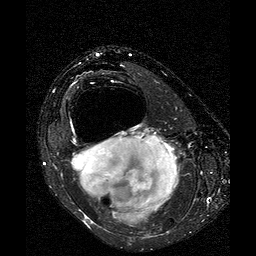
MRI of an extremity soft-tissue mass, one axial slice; position 20 of 25 along the scan axis; T2-weighted fat-saturated; 256 × 256 image matrix, field of view 160 × 160 mm. Female patient. Case-level facts recorded for this patient, not image findings: histological type: liposarcoma; site of the primary tumour: right thigh.
Structures marked on this image (expert manual segmentation):
- gross tumour volume (mass): bounding box [x1, y1, x2, y2] px = [70, 134, 181, 227]